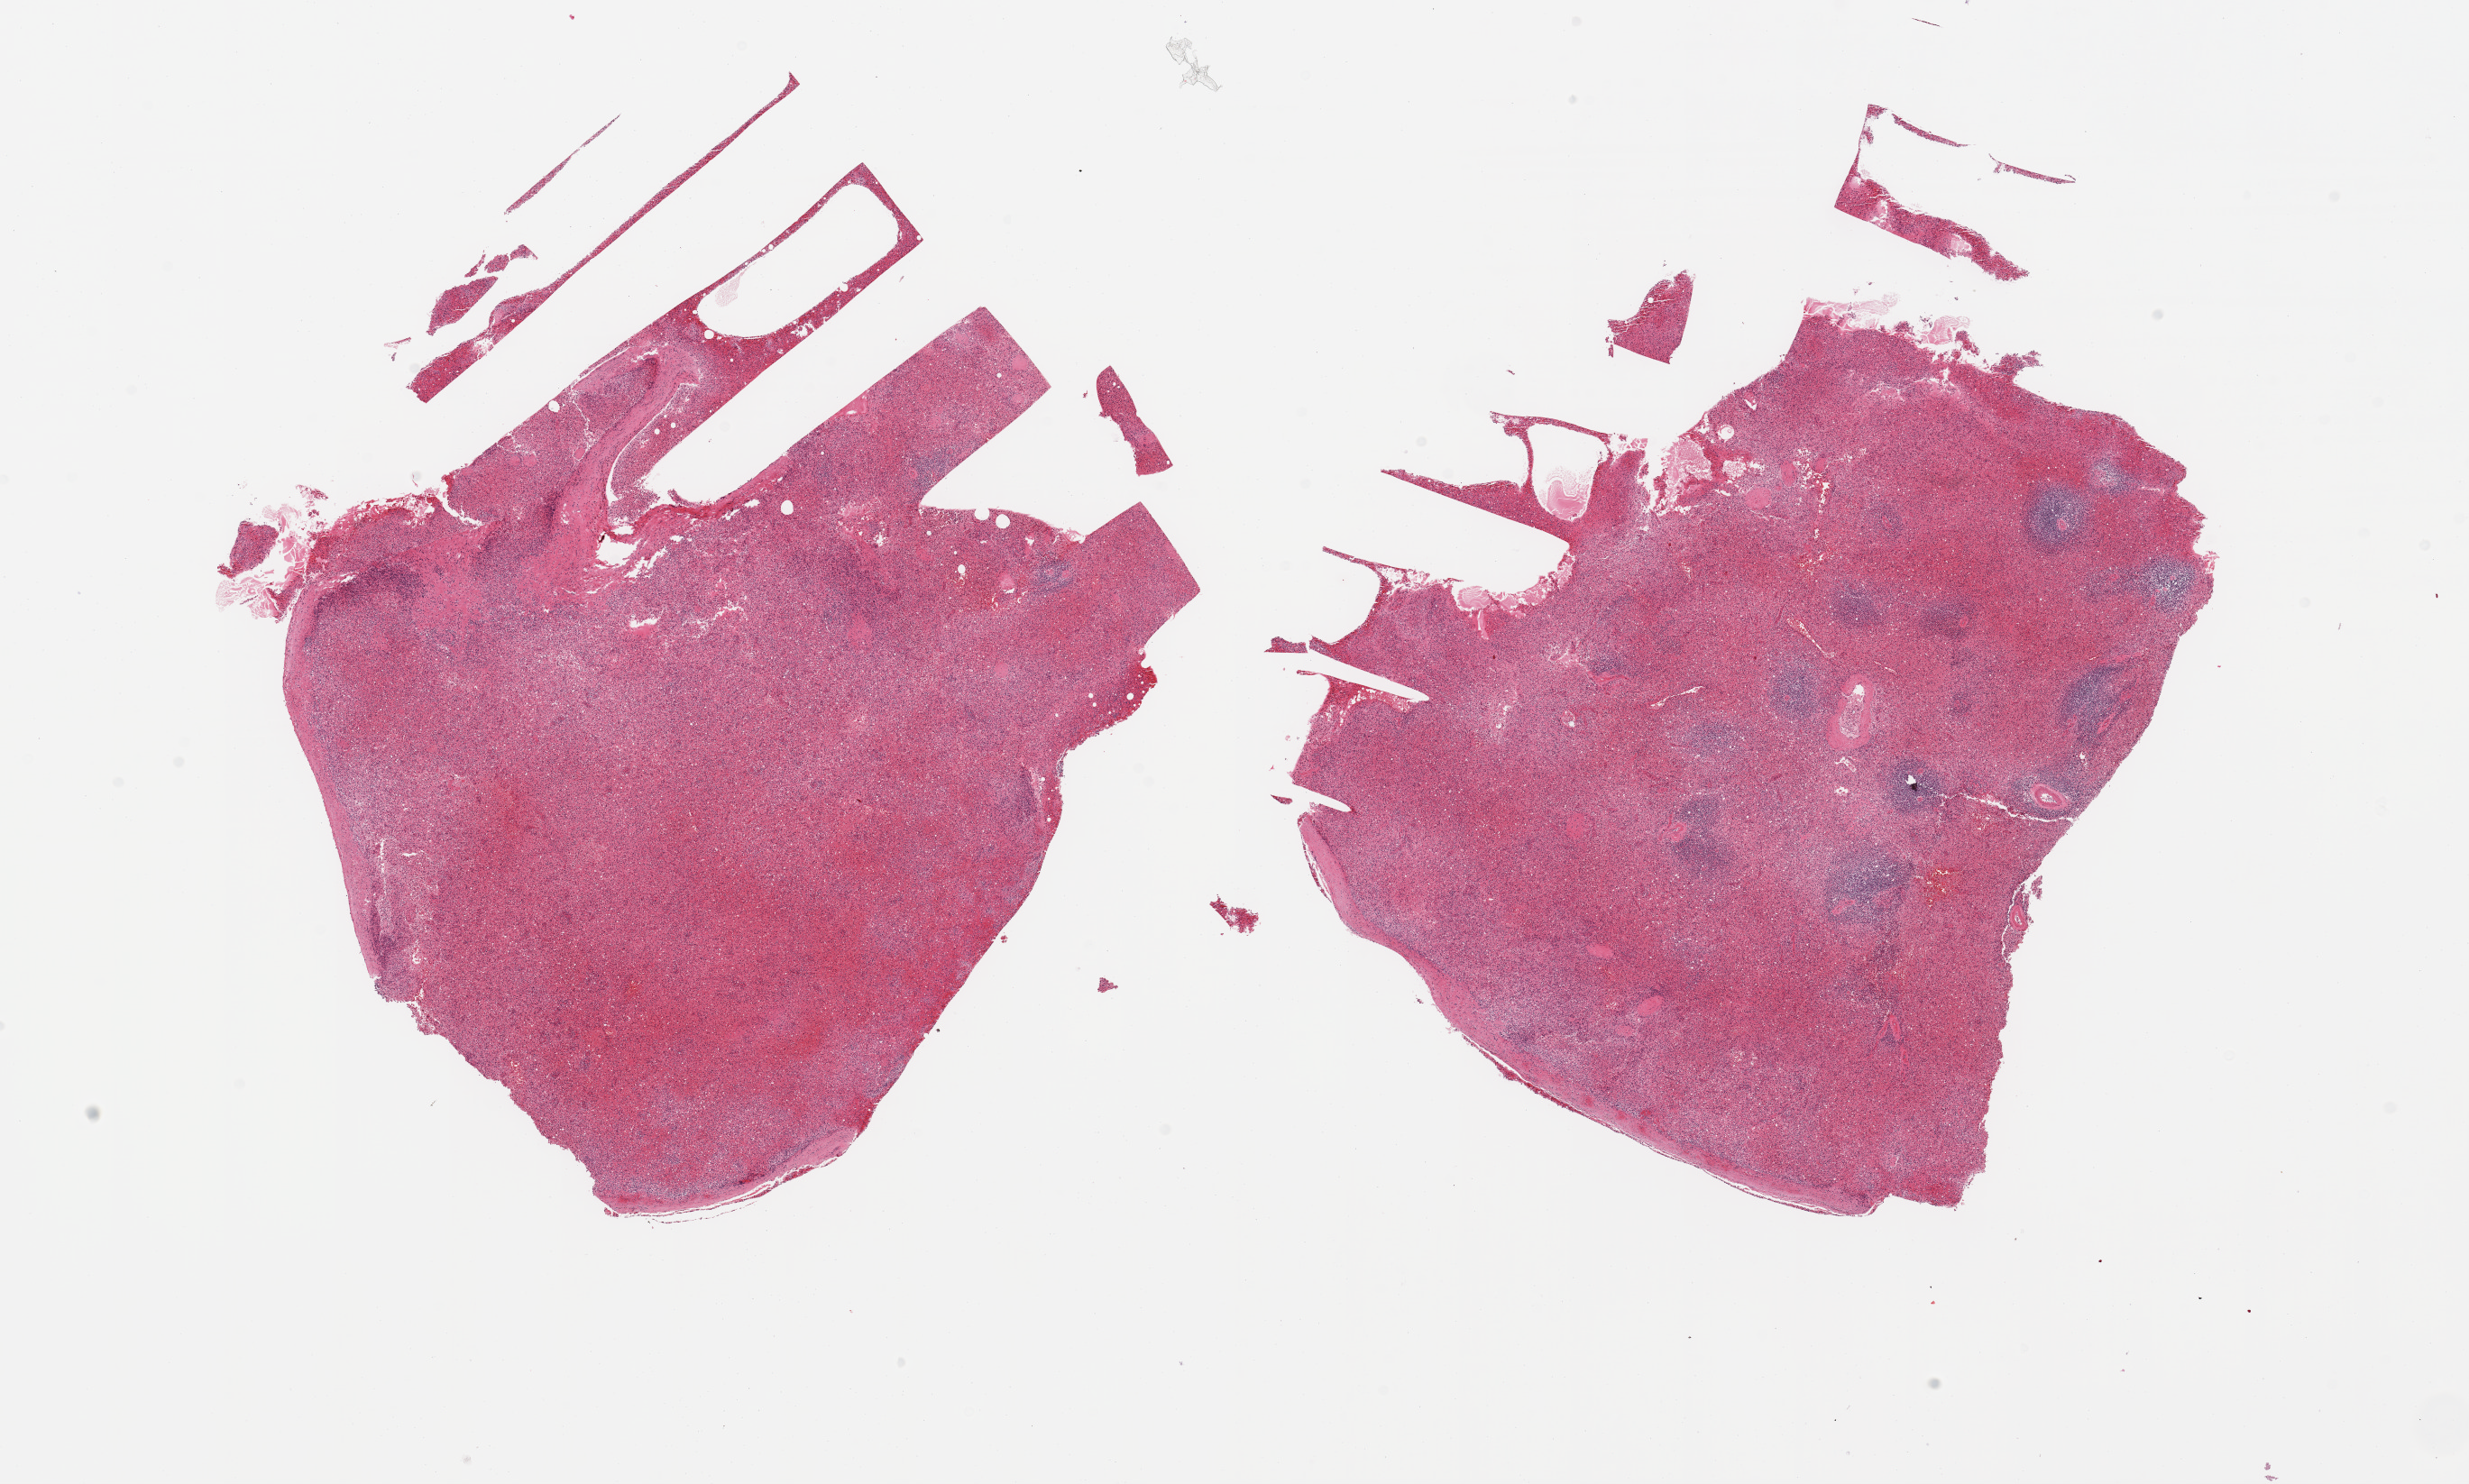
Digitized hematoxylin and eosin (H&E)-stained section, brightfield — a low-resolution overview of the entire scanned area, about 21.7 x 13.0 mm; PAXgene-fixed paraffin-embedded (PFPE) section; target tissue: spleen; donor tissue sample.
Pathologist's review note for this sample: 2 pieces, moderate-marked congestion.